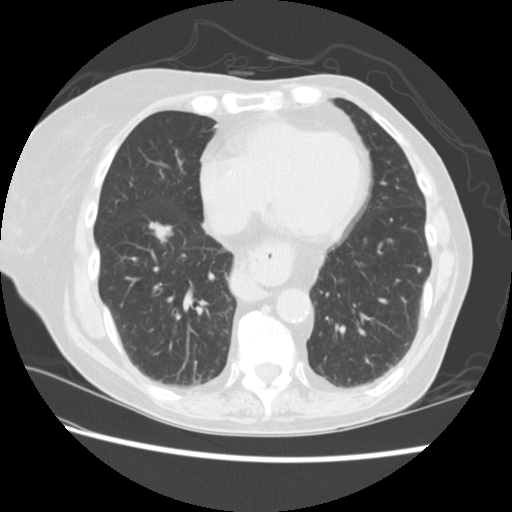
Low-dose screening chest CT, one axial slice. Position 73 of 224 along the scan axis. Reconstruction kernel STANDARD. 120 kVp. Lung window (W 1500 / L -600 HU). 512 × 512 image matrix.
Outlined on this slice (outlined manually by an expert reader):
- lesion 2 (tumor, lower lobe of right lung): bounding box (x1, y1, x2, y2) in pixels: (150, 222, 172, 242)